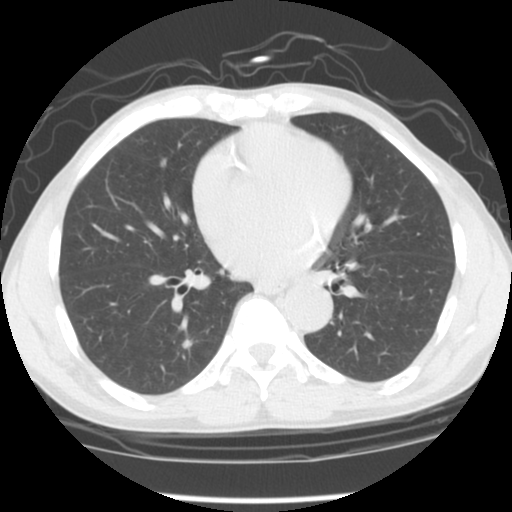
Low-dose screening chest CT, axial slice; second screening round (one year after baseline); lung window (W 1500 / L -600 HU); 2.5 mm slice thickness; standard (soft-tissue) reconstruction kernel (STANDARD). Male participant, aged 58 years at enrolment. Current smoker at enrolment.
• Expert-annotated lung lesion, box from (x=168, y=328) to (x=203, y=360) px.
• Screening reader's record for this exam (one nodule recorded; not confirmed to be the boxed lesion): non-calcified nodule or mass ≥4 mm, left upper lobe, 10 × 10 mm, poorly defined margins, ground glass attenuation, pre-existing on the prior screen: yes; interval growth: no.
• Note: the box lies in the patient's right hemithorax on this image, whereas the reader's record names the left lung; they may be different findings.
• Later outcome: lung cancer diagnosed 684 days after this screen — adenocarcinoma, NOS, right lower lobe, poorly differentiated (G3), stage IIIA (AJCC 6th edition), 15 mm at pathology.